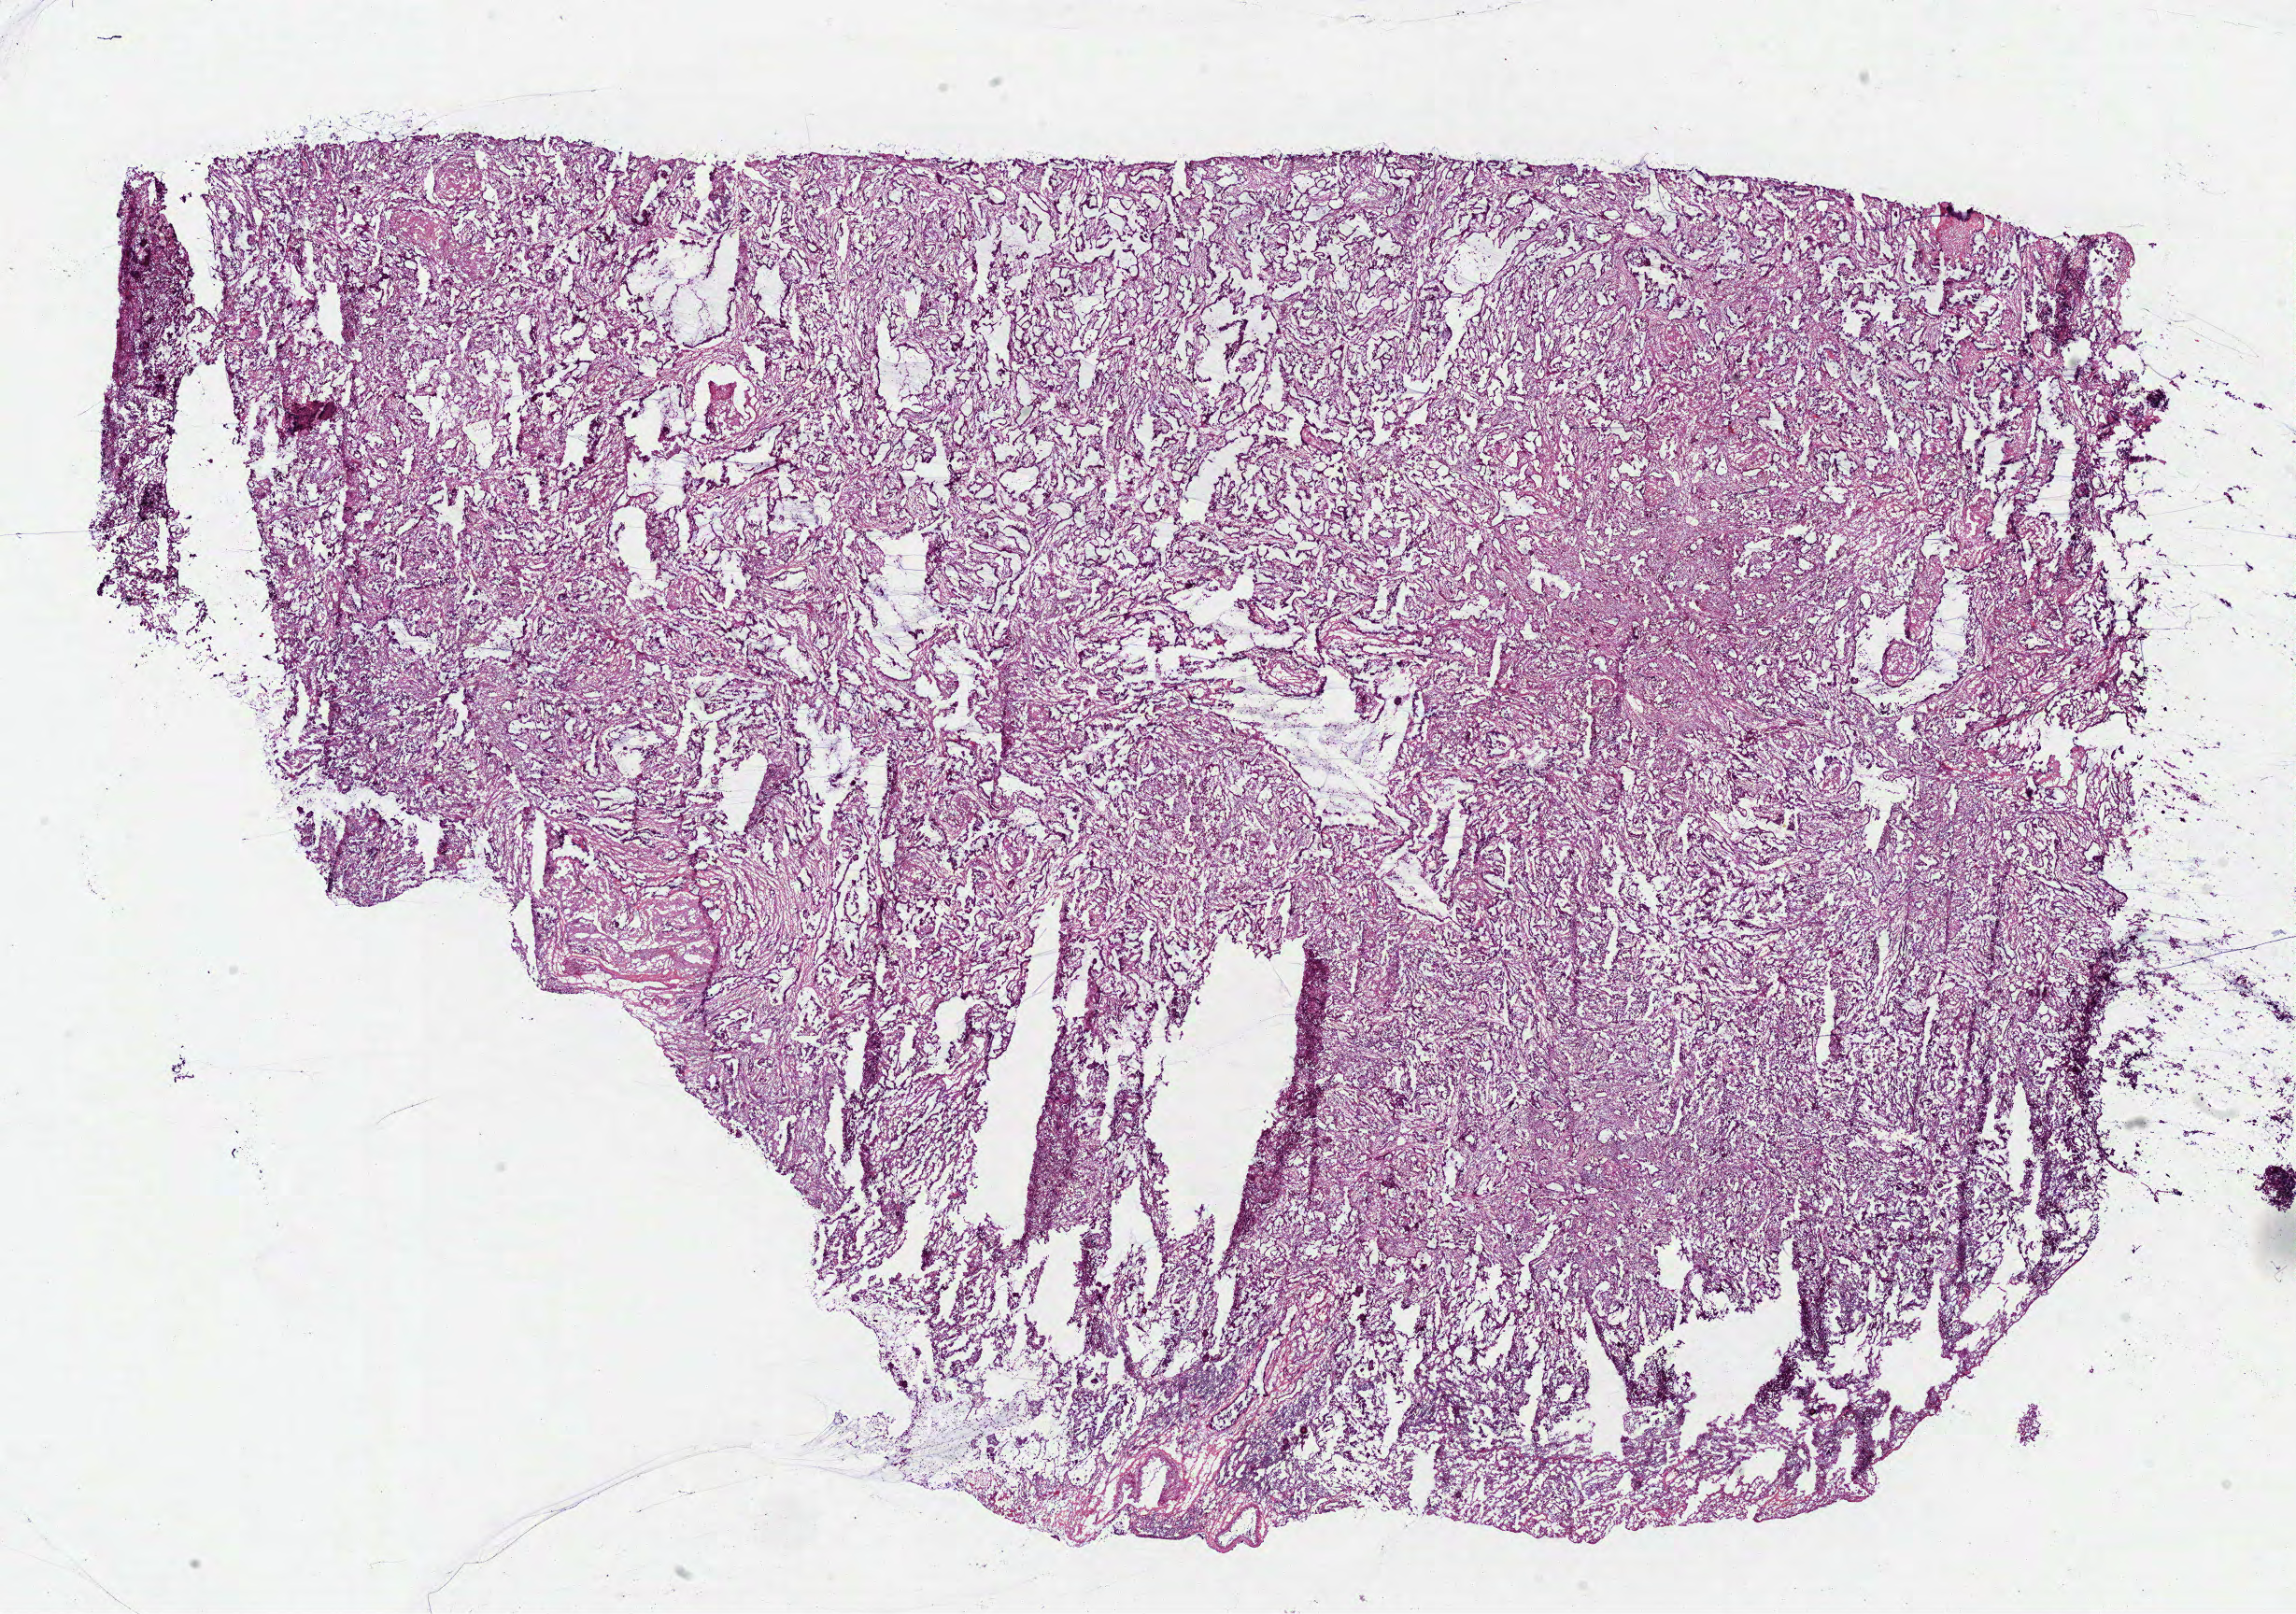
H&E-stained whole-slide image, low-resolution overview of the scanned area, about 19.8 x 13.9 mm. Frozen section from the top of the tissue portion. Primary tumour sample from the lung. Female patient; age at initial diagnosis 63 years. Composition of this section per pathologist review: tumour cells 85%, tumour nuclei 80%, normal cells 0%, stromal cells 15%, necrosis 0%.
Diagnosis: Mucinous adenocarcinoma (lower lobe, lung). AJCC pathologic stage: IIB. Laterality: left.